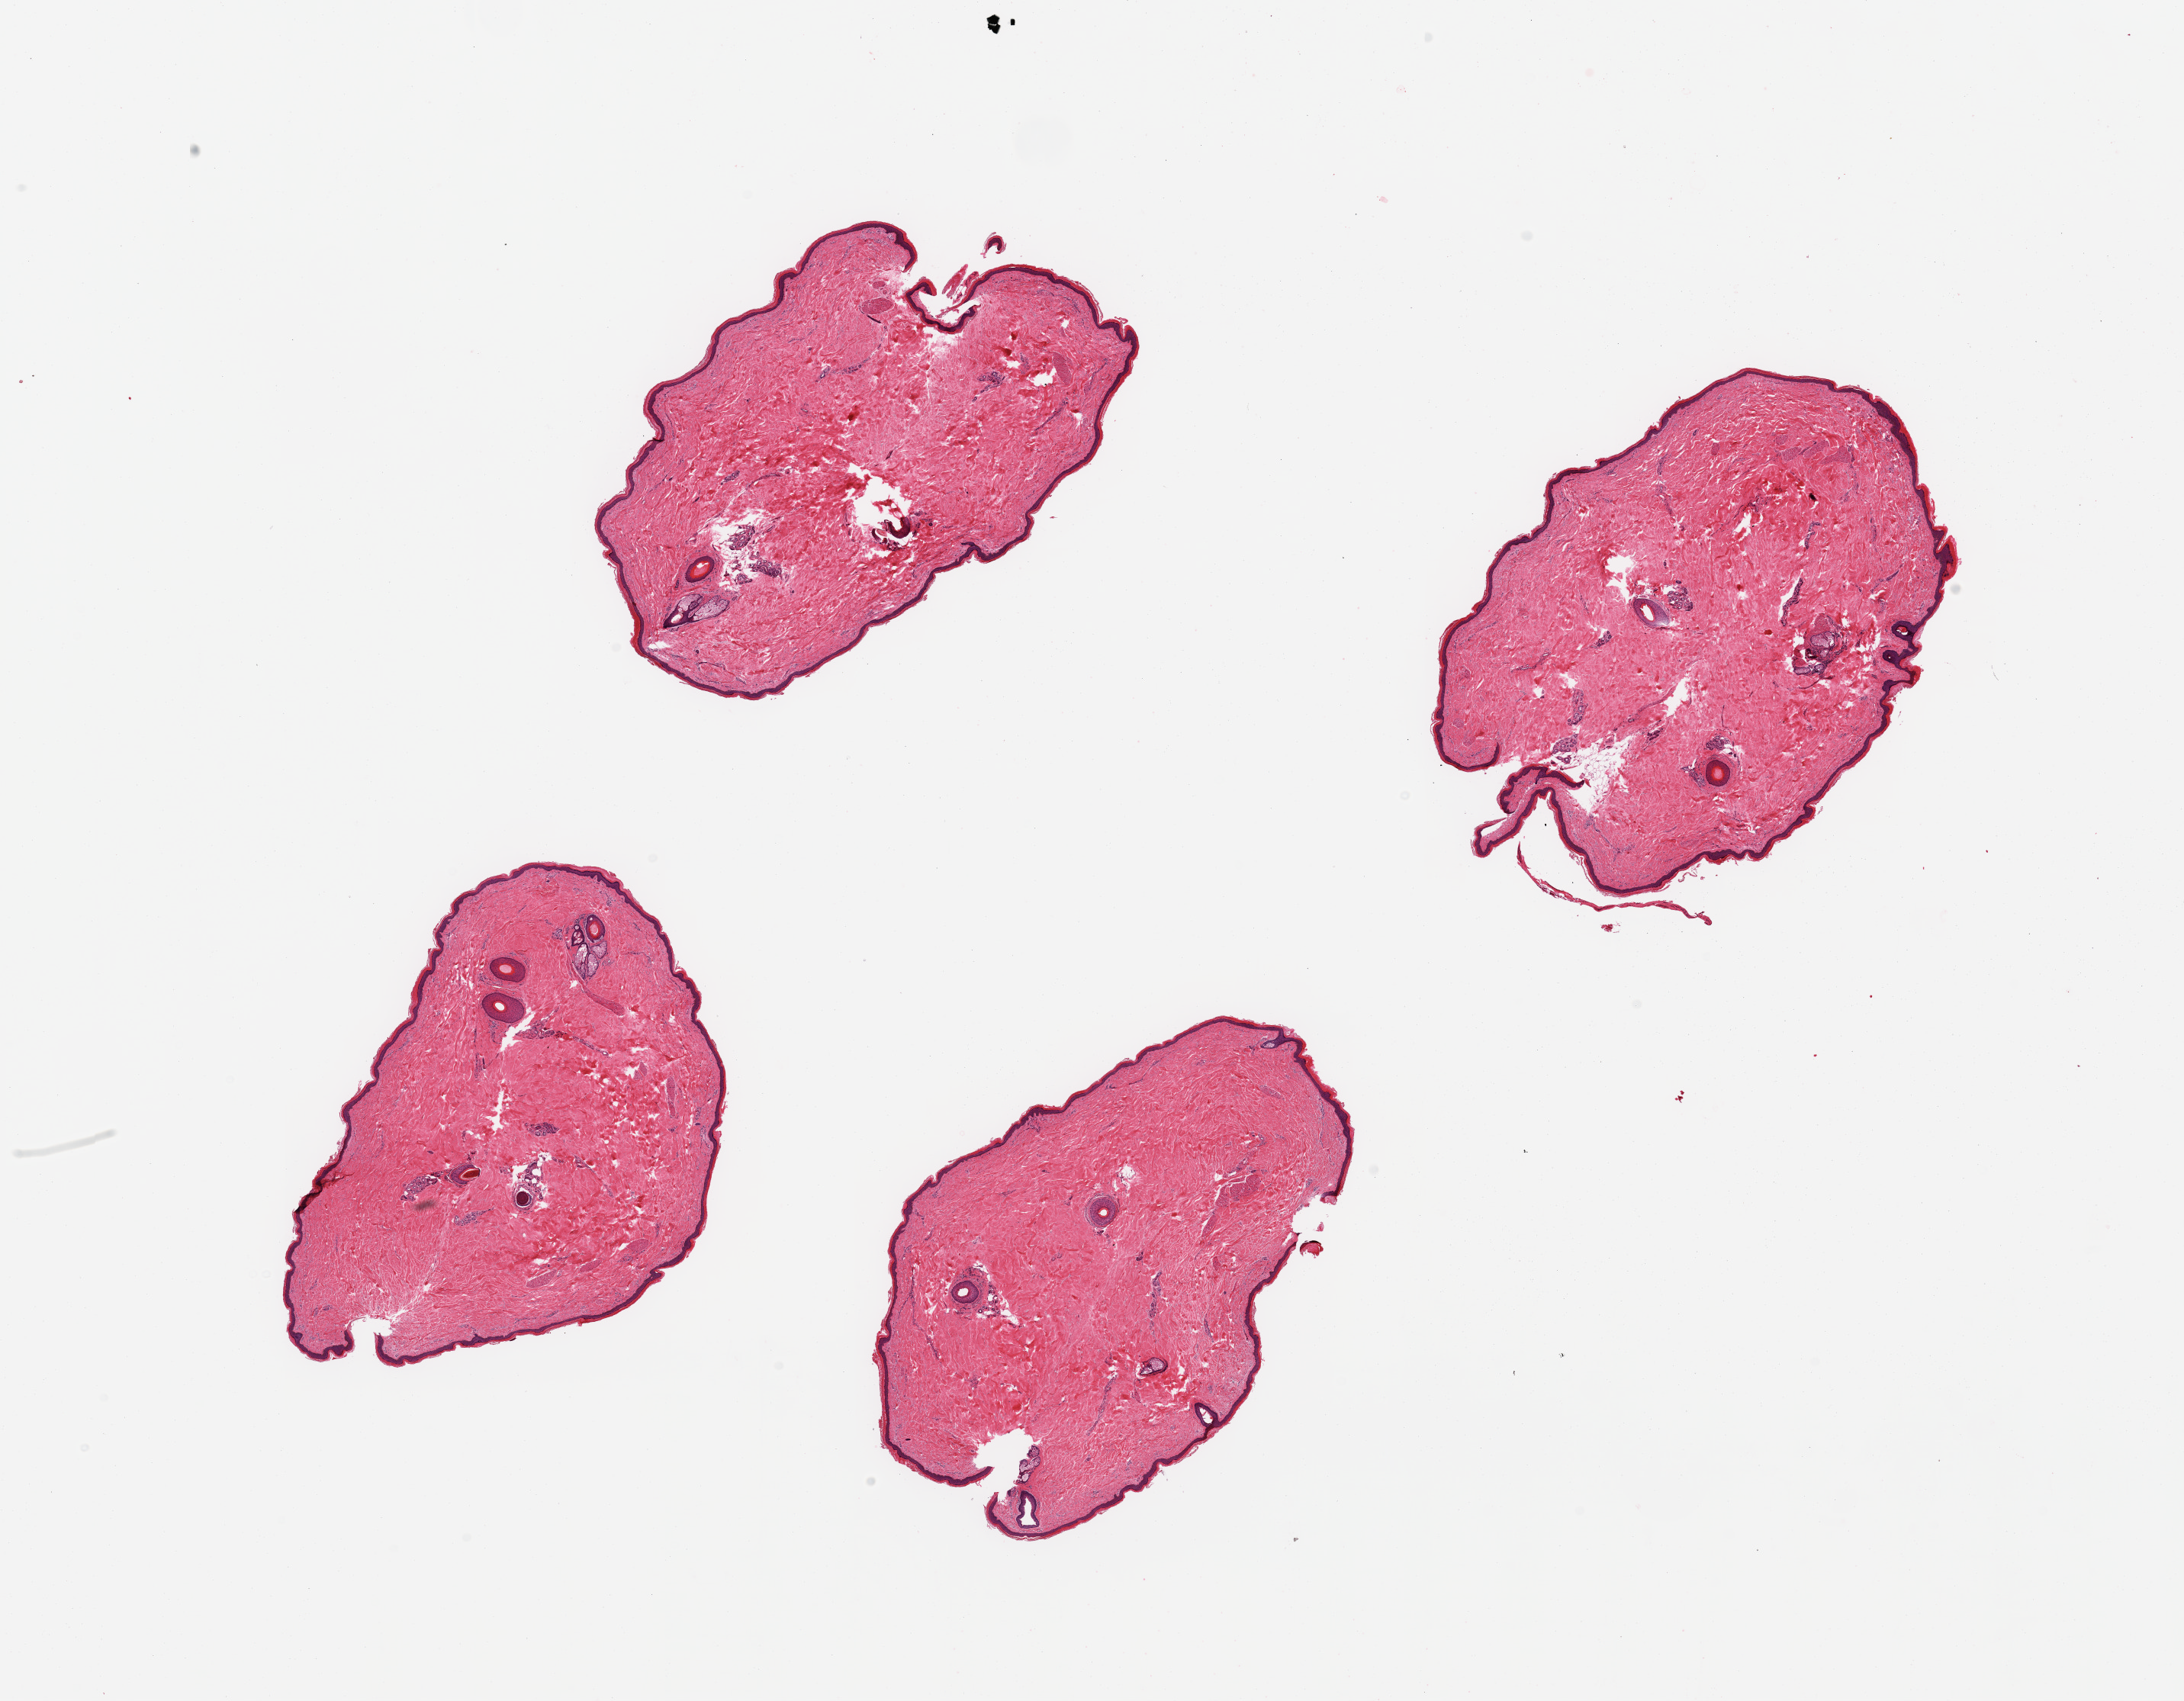
Digitized hematoxylin and eosin (H&E)-stained section, shown as a low-resolution overview of the whole scanned area (about 22.6 x 17.6 mm, from a 20x scan). PAXgene-fixed paraffin-embedded (PFPE) section. Sampled site (target tissue): skin of lower leg. Tissue donor sample. Male donor.
- pathologist's review note for this sample: 4 pieces; tangentially cut hair bearing skin; ~34 microns thick epidermis